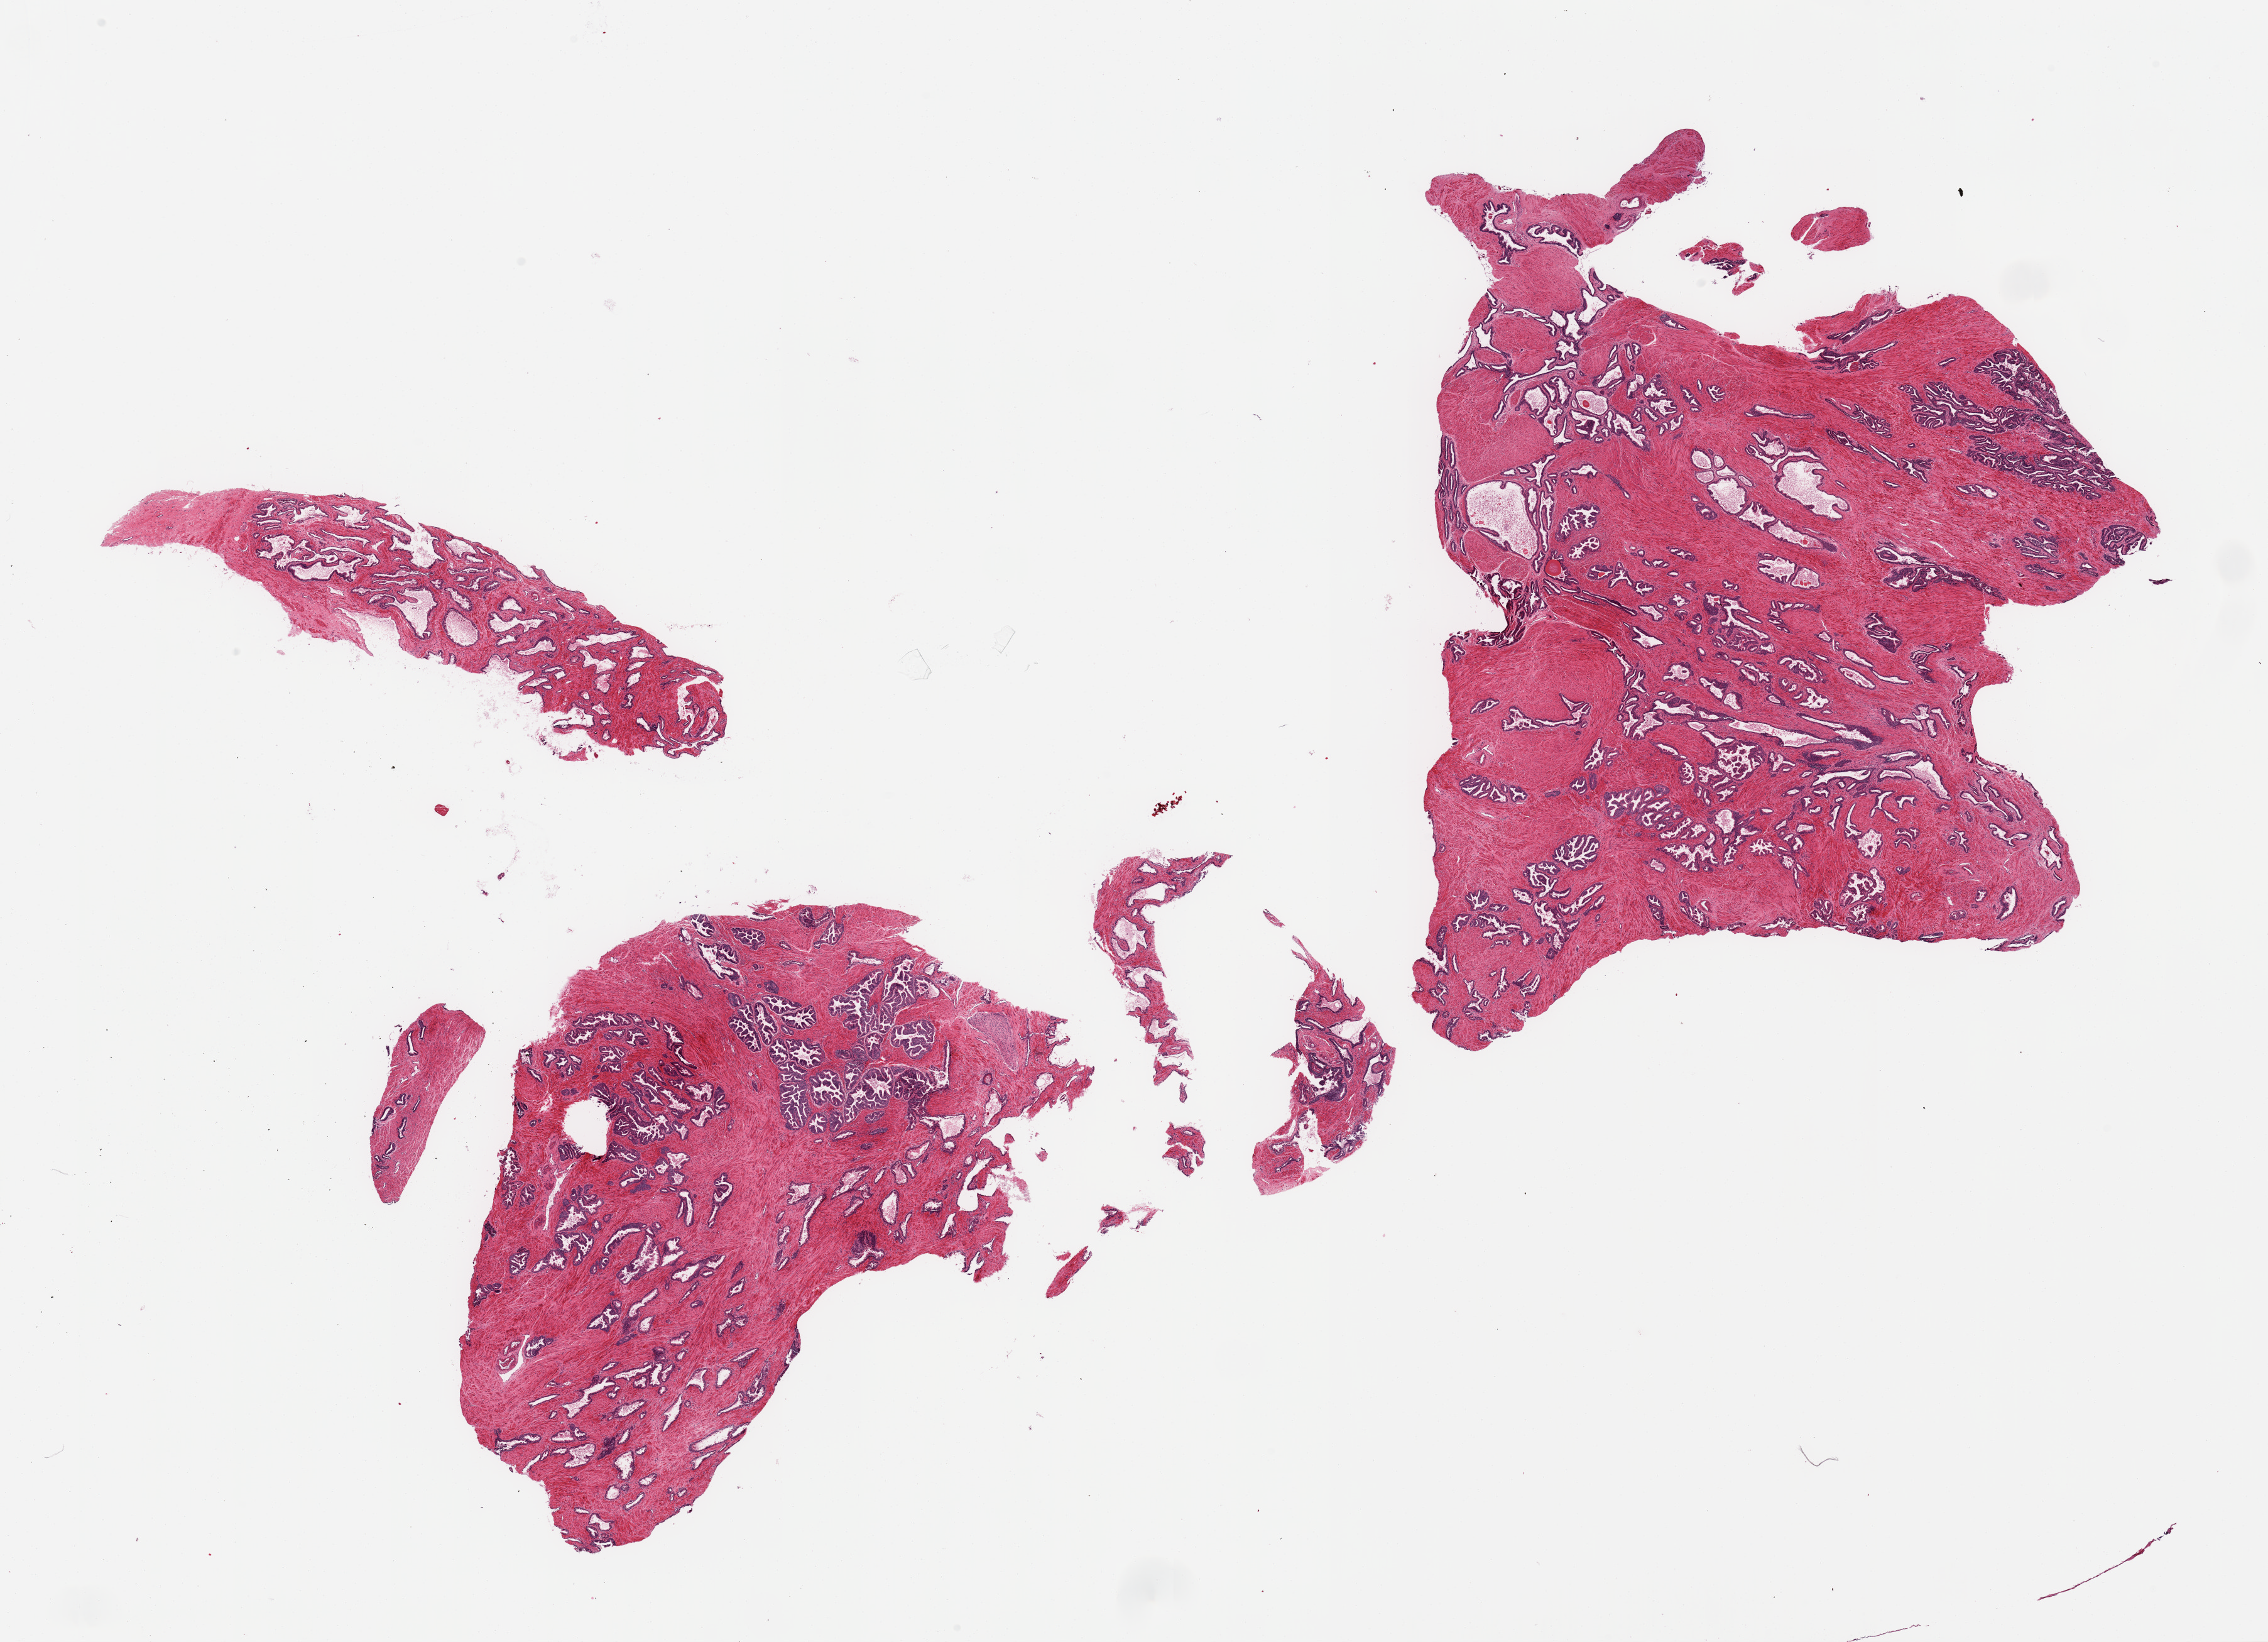
Digitized haematoxylin and eosin-stained section — low-resolution overview of the scanned area, about 28.5 x 20.7 mm, PAXgene-fixed, paraffin-embedded tissue, sampled site (target tissue): prostate, donor tissue sample. Male donor.
• review note (as recorded): 2 pieces; no lesions